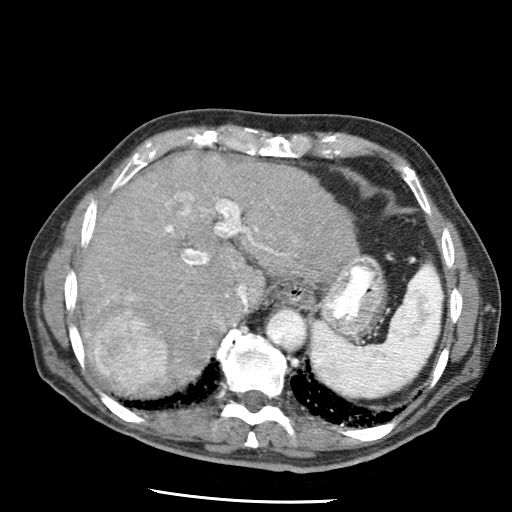
Contrast-enhanced abdominal CT (liver protocol), one axial slice; position 50 of 79 along the scan axis; reconstruction kernel STANDARD; soft-tissue window (W 400 / L 40 HU); 512 × 512 image matrix. From the clinical record (not read from this slice): diagnosis: hepatocellular carcinoma (patient treated with transarterial chemoembolisation; whether this scan precedes or follows treatment is not stated here); TNM stage (as recorded): Stage-IIIA; Child-Pugh class: A; tumour differentiation: moderately differentiated; tumour size: 7 cm.
Annotated regions visible in this slice (semi-automatic segmentation, software-assisted and operator-edited):
- abdominal aorta: bounding box <268,310,306,350> (left, top, right, bottom; pixels)
- liver parenchyma outside the tumour (the mass and vessels are separate outlines, so this box may not span the whole liver): <76,152,357,394>
- mass: <93,311,167,391>
- liver vessels: <86,158,295,336>